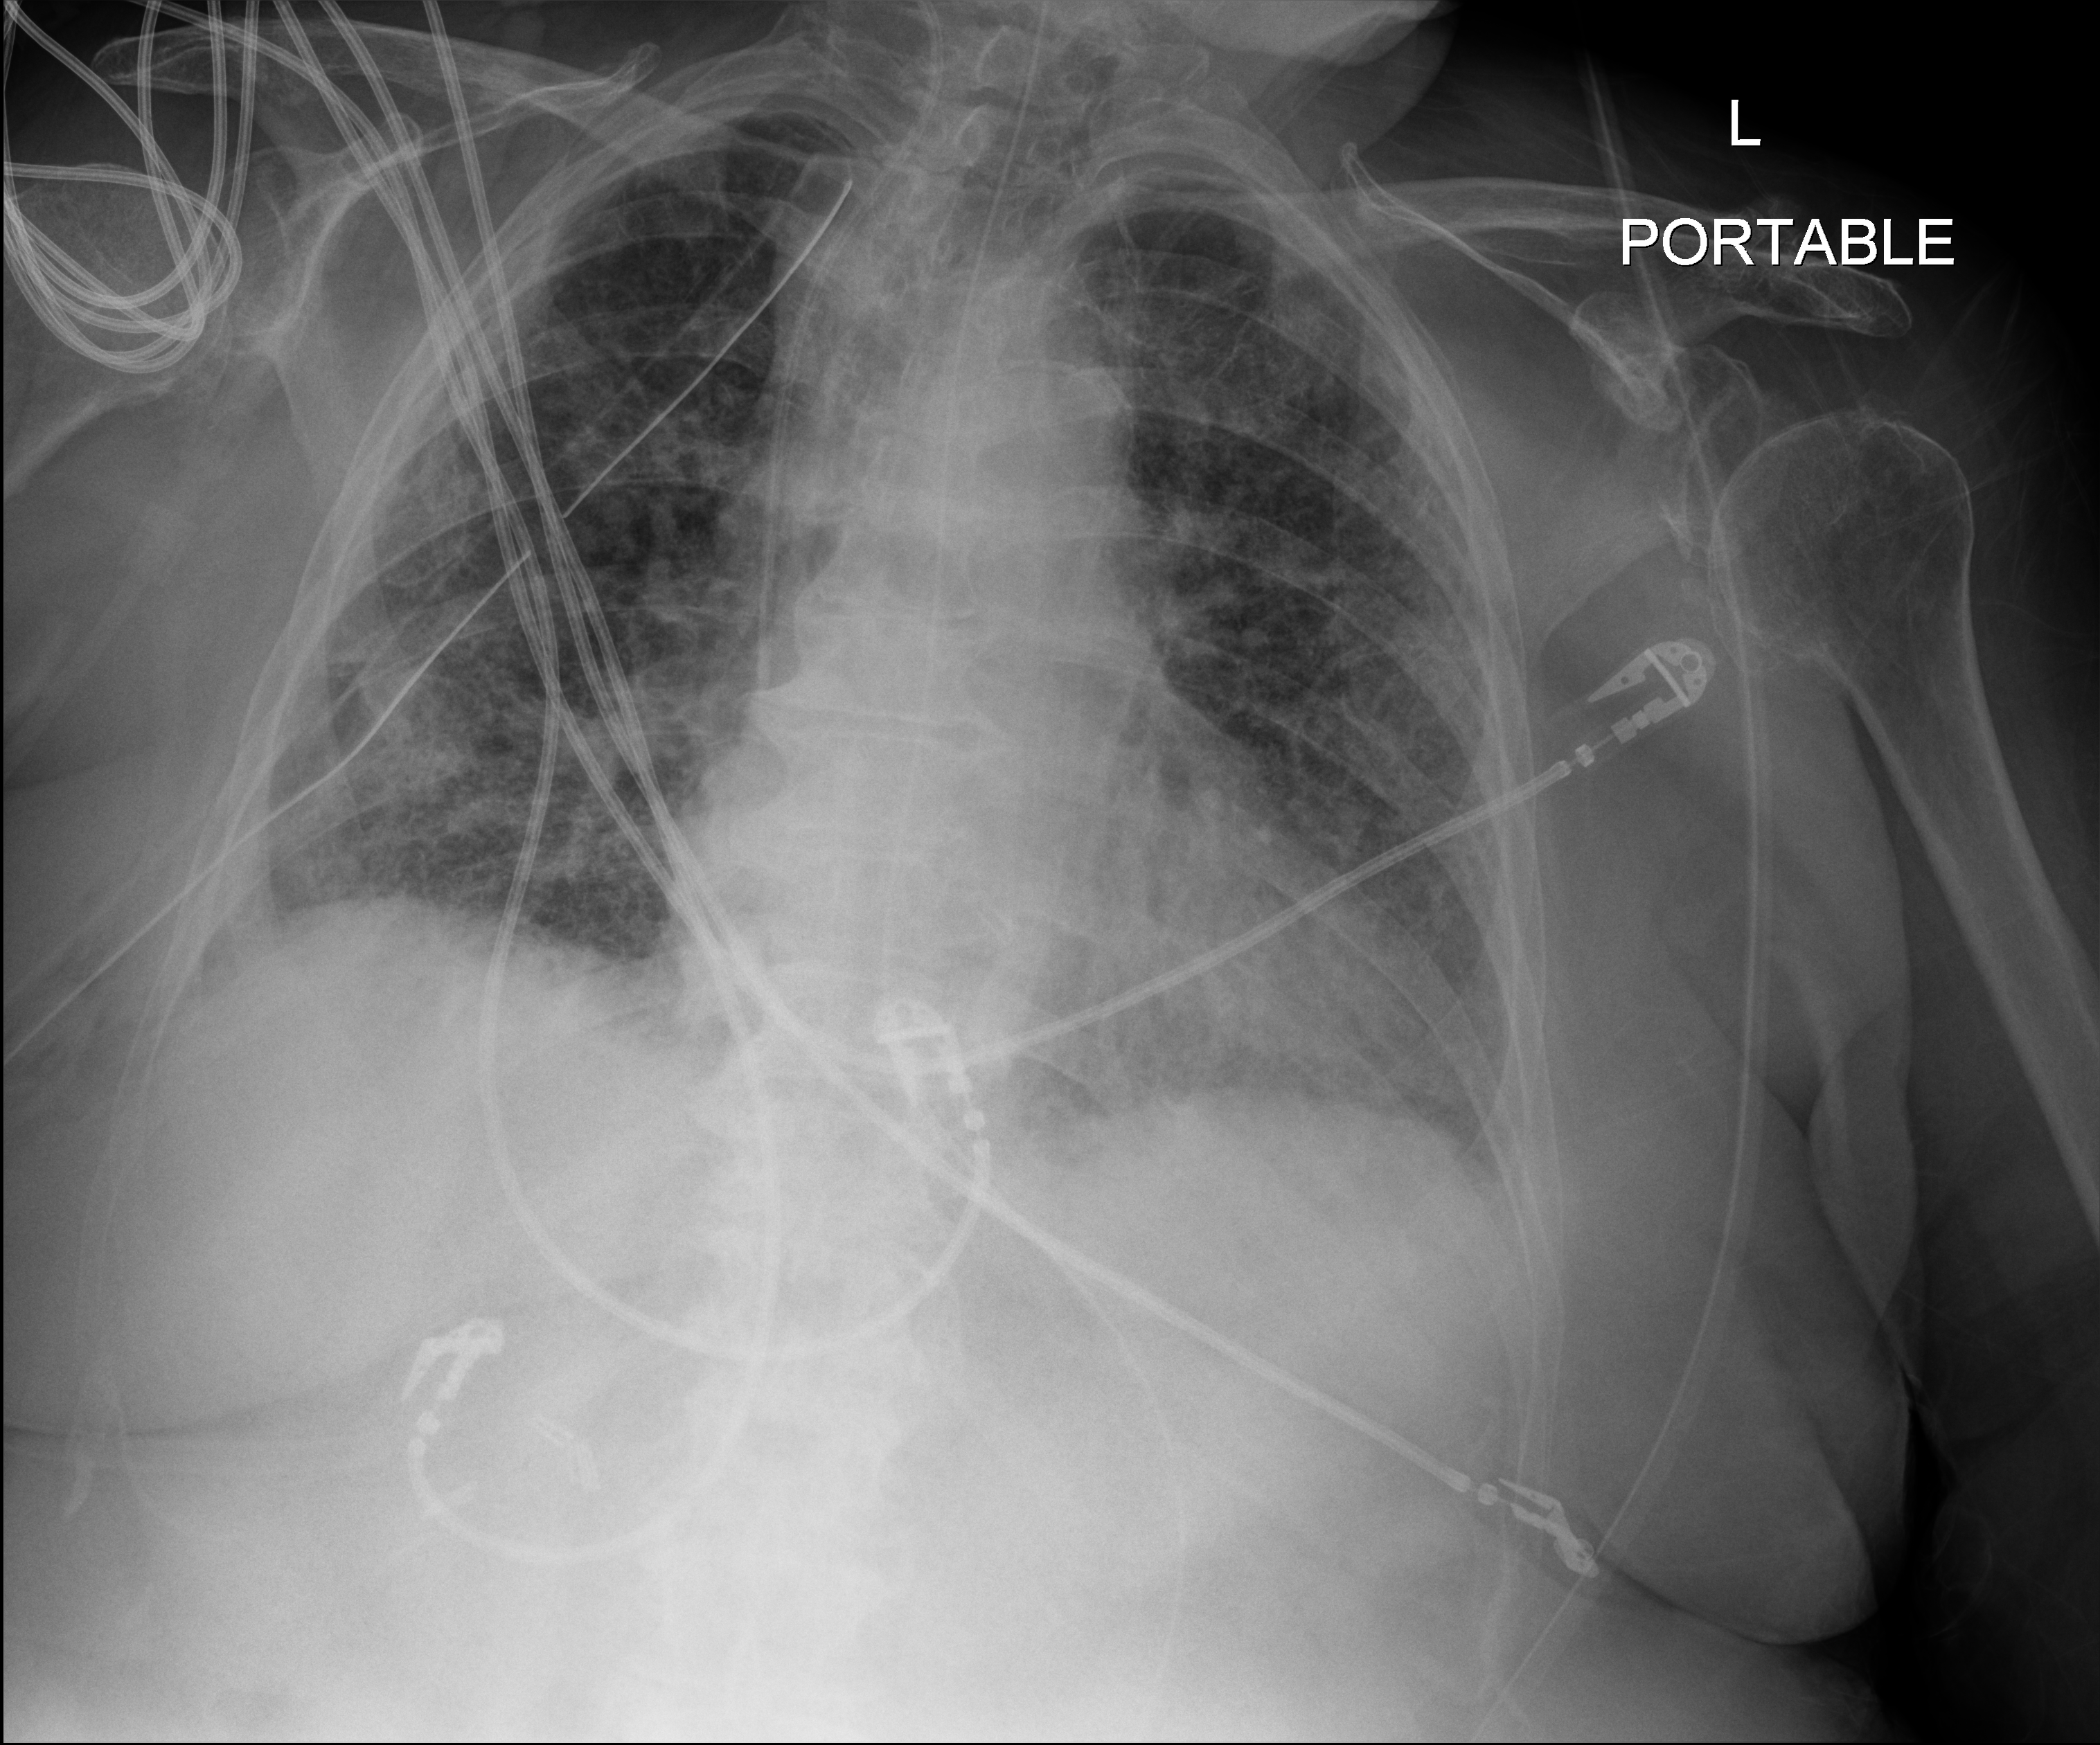
Bedside chest radiograph (digital radiography), anteroposterior (AP) projection. Patient hospitalised with COVID-19; female, aged 75–90 years.
Hospital-stay facts (about this admission, not read from this image; timing relative to this image not recorded): mechanically ventilated during this hospital stay: yes; admitted to intensive care during this hospital stay: no; chronic kidney disease (admission record): no.